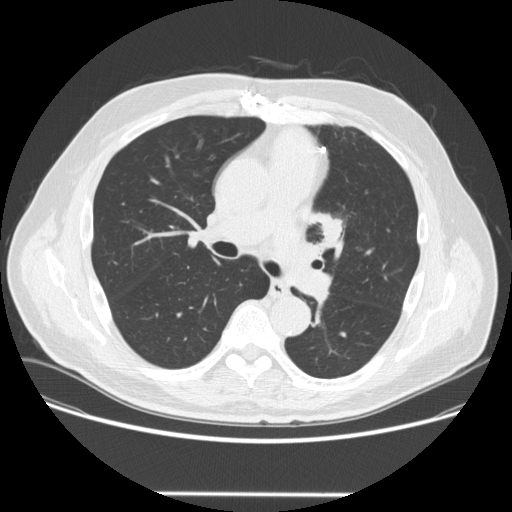
Low-dose screening chest CT, one axial slice; slice 158 of 253 in the series (ordered by position); lung window (W 1500 / L -600 HU); 512 × 512 image matrix, field of view 400 × 400 mm.
Annotated regions visible in this slice (outlined manually by an expert reader):
- lesion 1 (tumor, upper lobe of left lung): bounding box <321,218,342,244> (left, top, right, bottom; pixels)